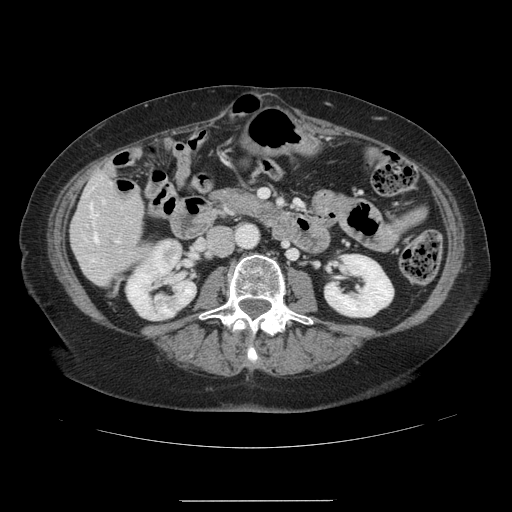
Contrast-enhanced abdominal CT, one axial slice; soft-tissue window (W 400 / L 40 HU); 2.5 mm slice thickness; 512 × 512 image matrix. Female patient, age 74 years. Case-level facts recorded for this patient, not image findings: diagnosis: colorectal cancer liver metastases, imaged before liver resection; multiple liver metastases: yes; largest metastasis: 7 cm.
Annotated regions visible in this slice (expert manual segmentation):
- hepatic veins: bounding box <90,205,98,242> (left, top, right, bottom; pixels)
- liver: <72,173,144,286>
- planned liver remnant (the part of the liver to remain after resection): <79,173,144,286>
- portal vein (with intrahepatic branches): <103,201,118,242>